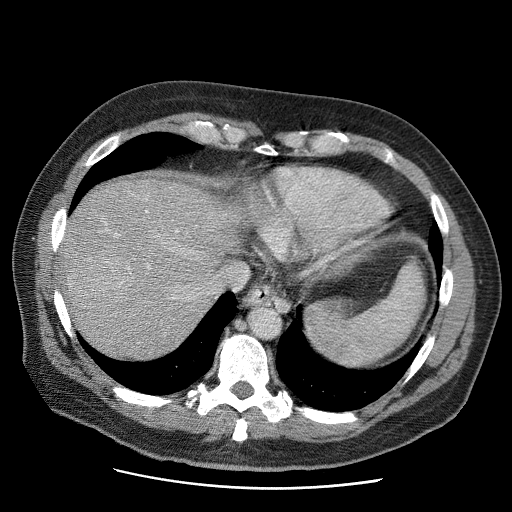
Contrast-enhanced abdominal CT (liver protocol), one axial slice; slice 52 of 81 in the series (ordered by position); reconstruction kernel STANDARD; 120 kVp; soft-tissue window (W 400 / L 40 HU); 512 × 512 image matrix, field of view 380 × 380 mm. From the clinical record (not read from this slice): diagnosis: hepatocellular carcinoma (patient treated with transarterial chemoembolisation; whether this scan precedes or follows treatment is not stated here); TNM stage (as recorded): Stage-IIIA; Child-Pugh class: A; tumour nodularity: multinodular; tumour size: 5.5 cm.
Structures marked on this image (semi-automatic segmentation, software-assisted and operator-edited):
- liver parenchyma outside the tumour (the mass and vessels are separate outlines, so this box may not span the whole liver): box from (x=54, y=178) to (x=265, y=358) px
- mass: (x=62, y=226)–(x=134, y=320)
- liver vessels: (x=145, y=210)–(x=189, y=297)